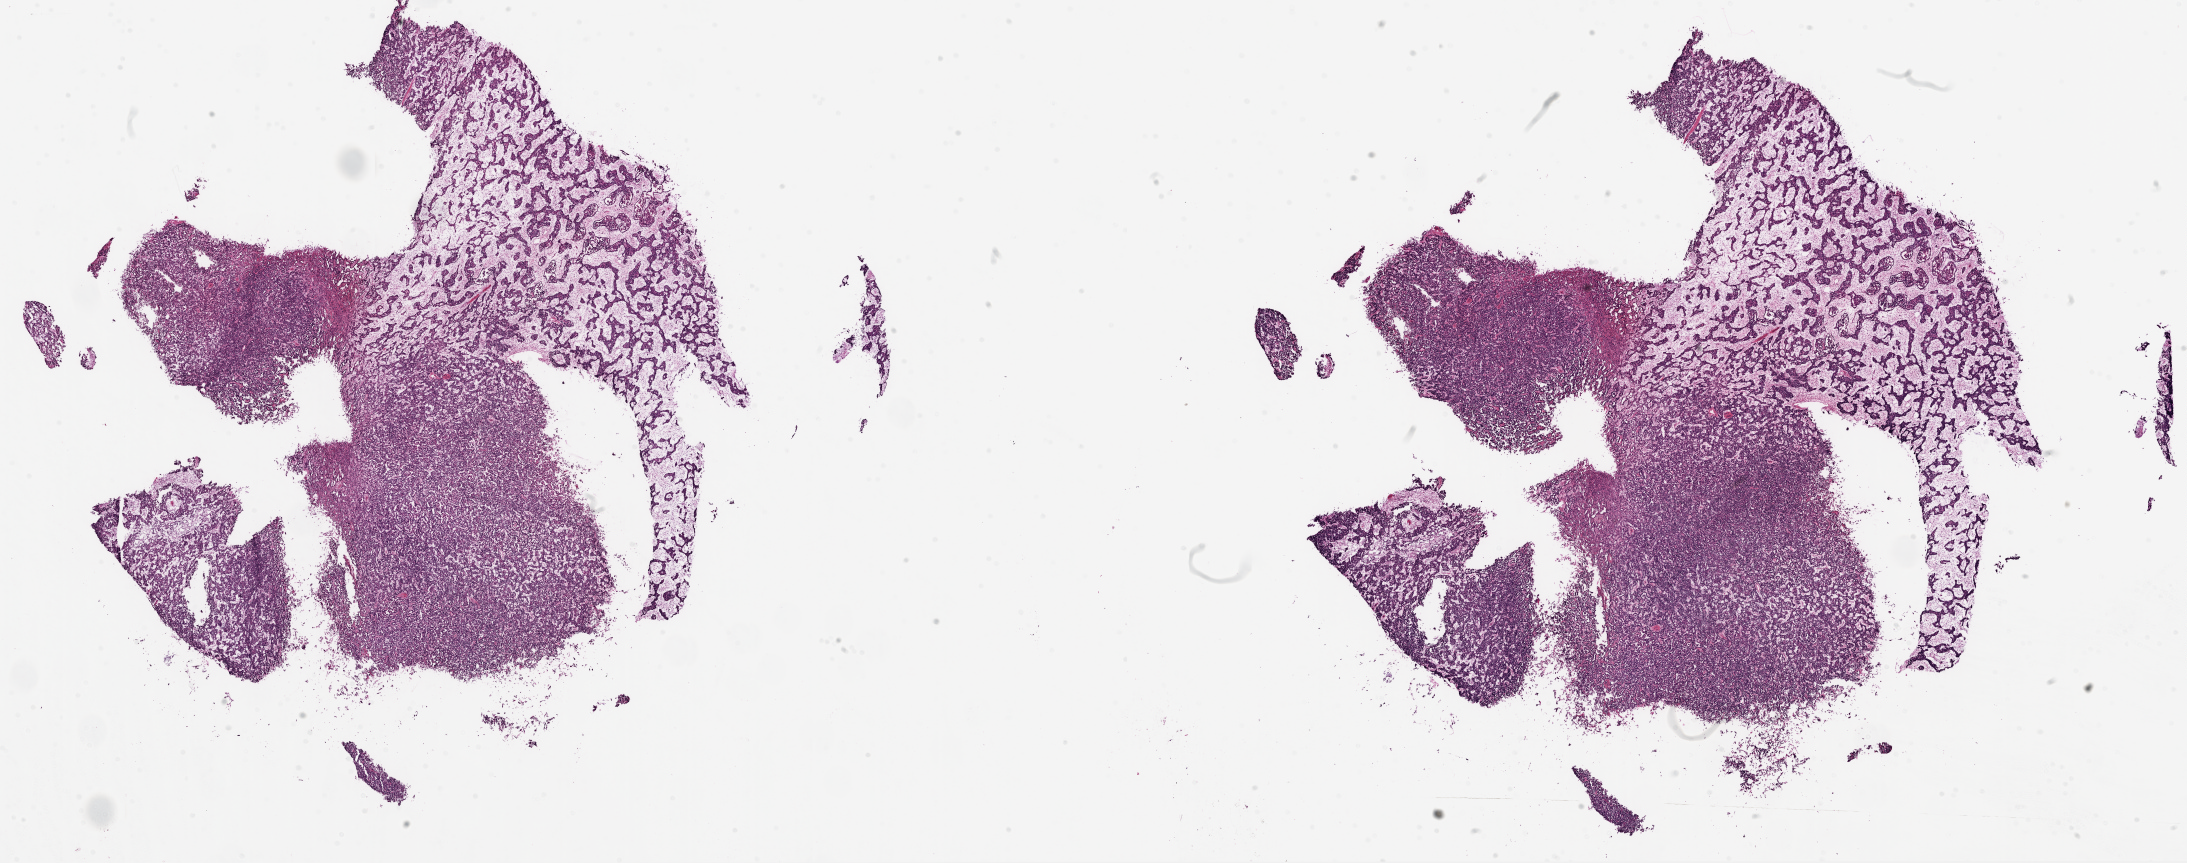
H&E whole-slide image, whole scanned area (about 35.1 x 13.9 mm, from a 20x scan) shown as a low-resolution overview, frozen section from the top of the tissue portion, sample: primary tumour, kidney. Female, age 38 years at initial diagnosis. Composition of this section per pathologist review: tumour cells 75%, tumour nuclei 80%, normal cells 0%, stromal cells 25%, necrosis 0%.
Diagnosis: Papillary adenocarcinoma, NOS. AJCC pathologic stage: I (6th edition). Laterality: right.